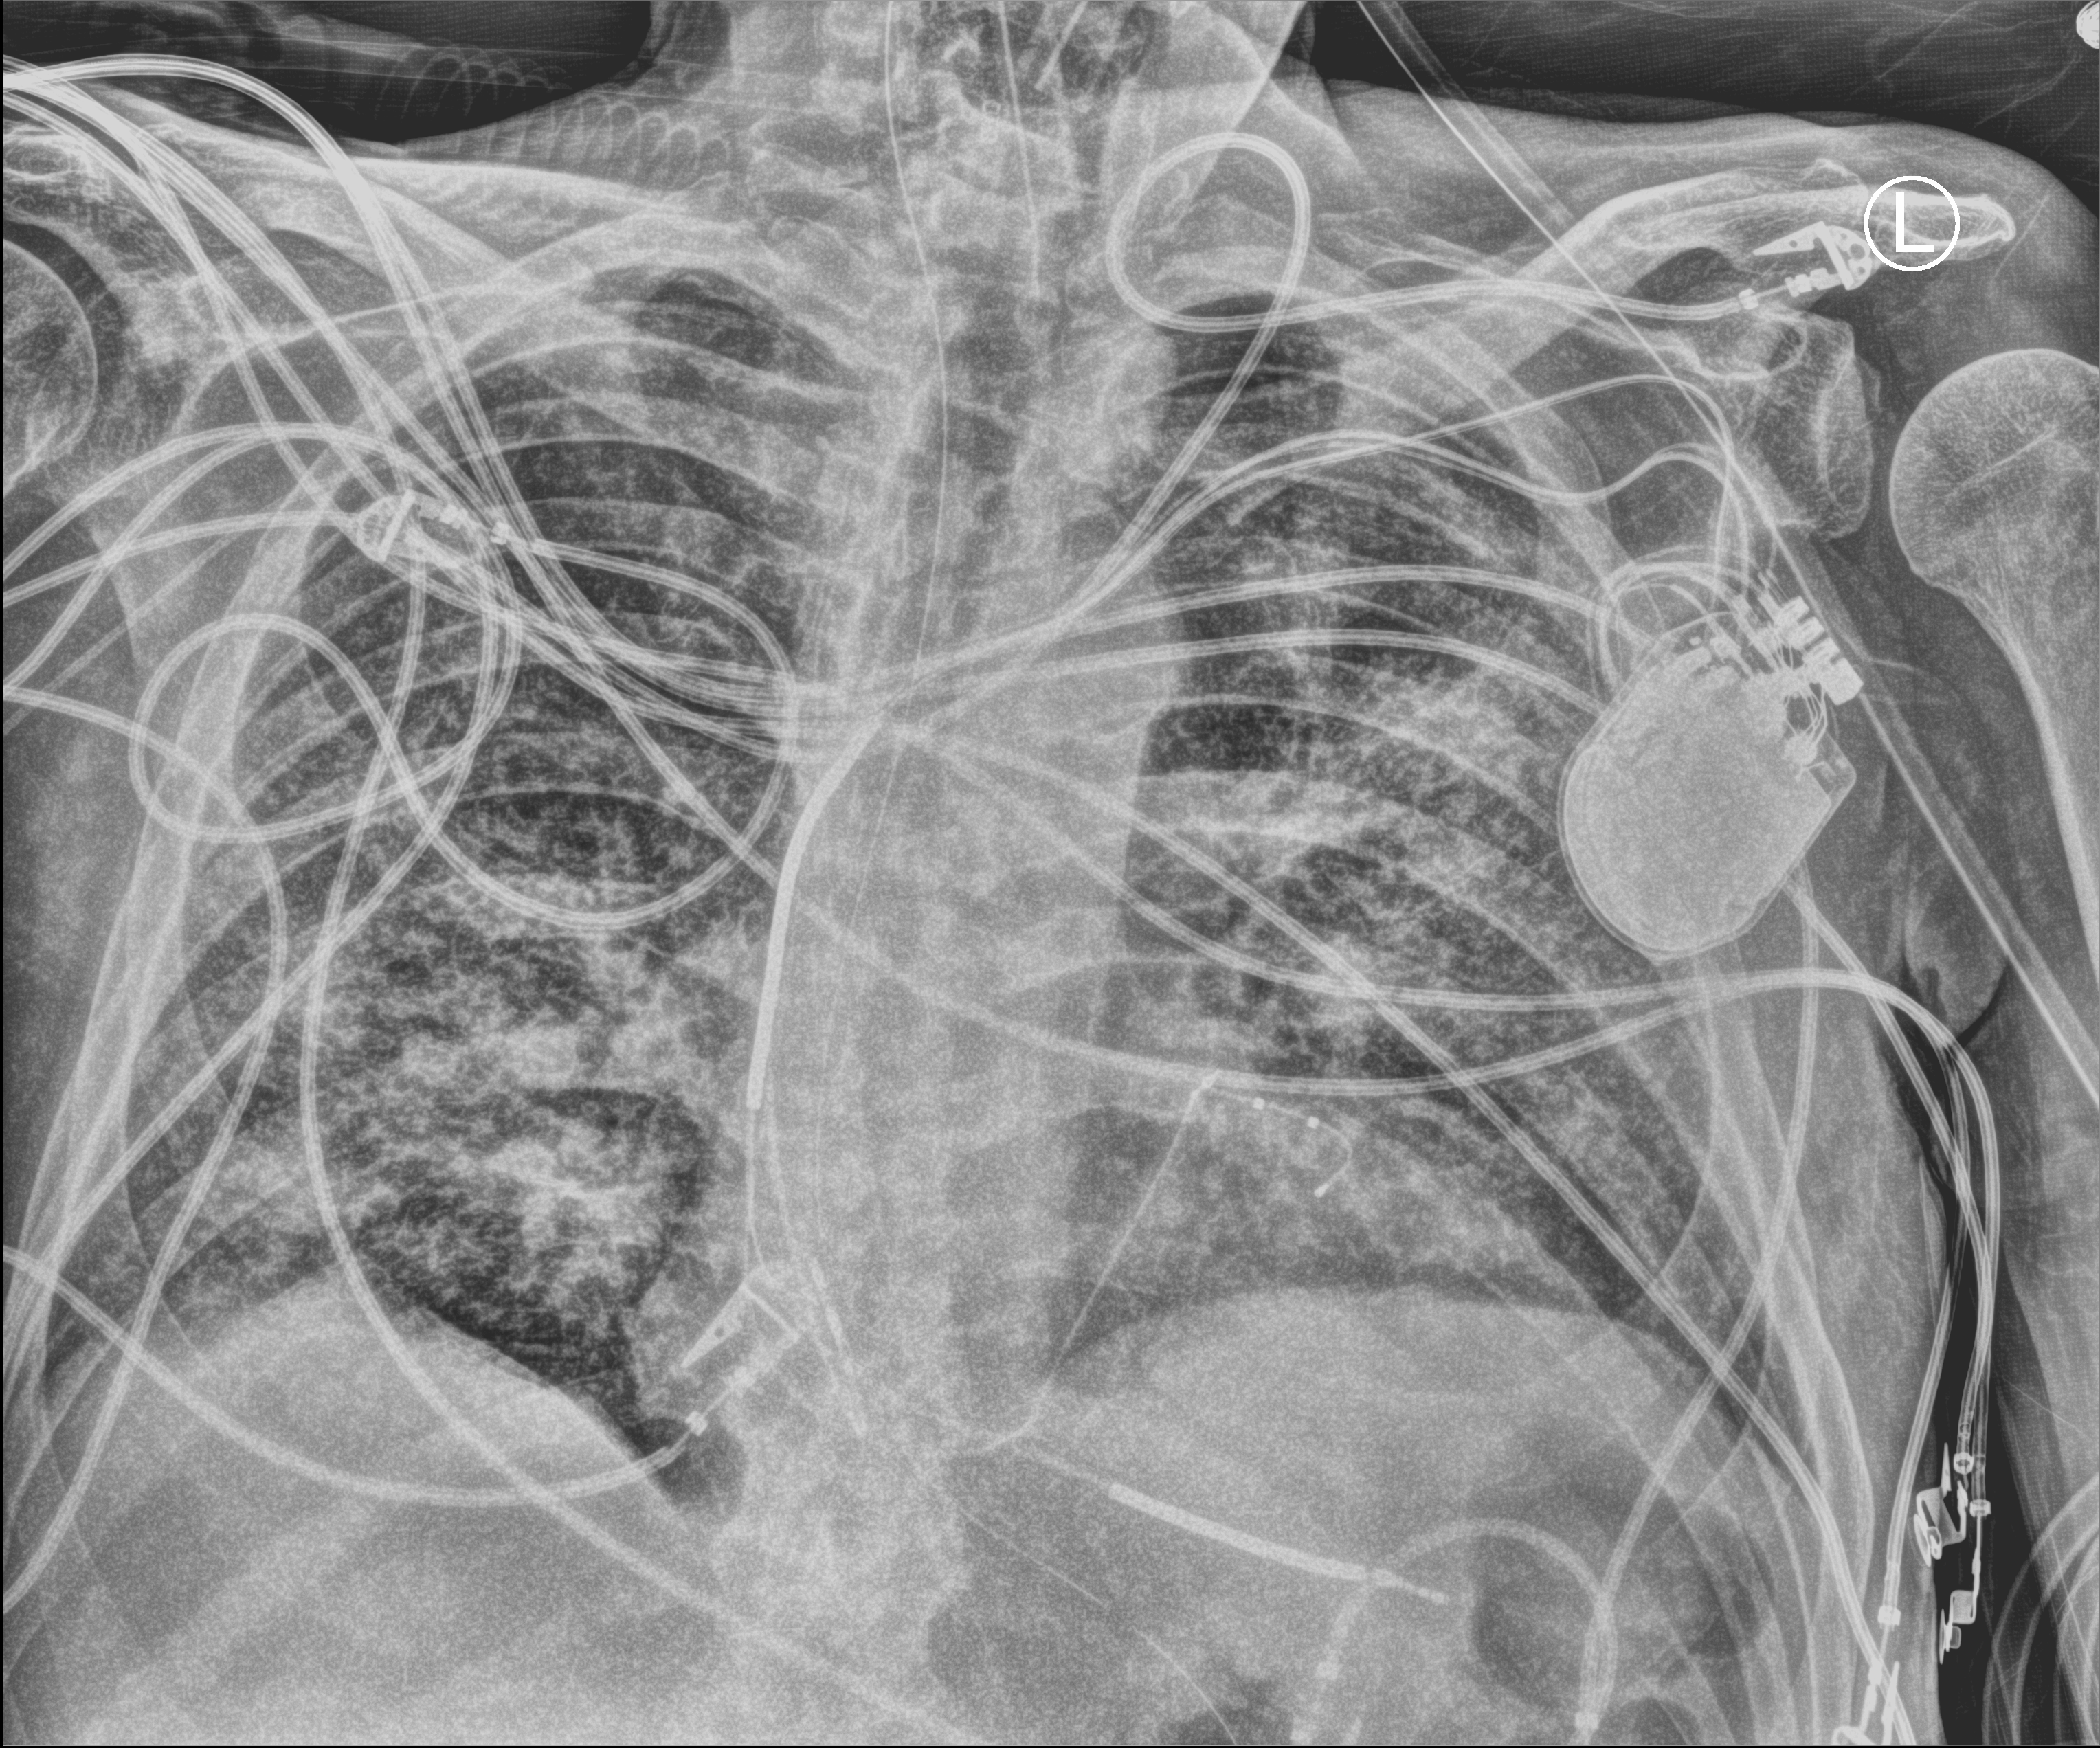
Bedside chest radiograph (computed radiography), anteroposterior (AP) projection. Male patient hospitalised with COVID-19, age 60–74 years.
Admission-level facts for this patient (not findings on this image; timing relative to this image not recorded):
- smoking status (admission record): former
- admitted to intensive care during this hospital stay: yes